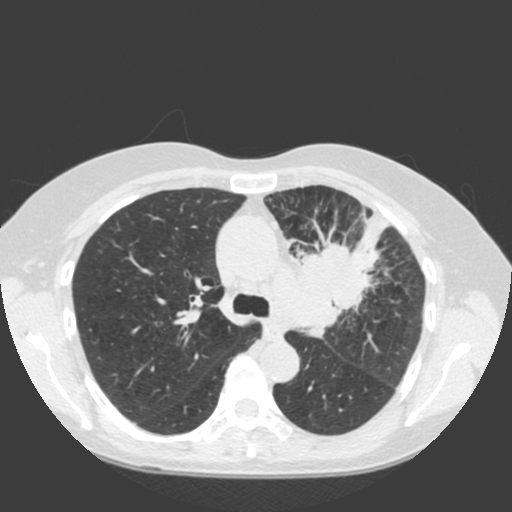
Low-dose screening chest CT, one axial slice; slice 128 of 184 in the series (ordered by position); 120 kVp; lung window (W 1500 / L -600 HU); 512 × 512 image matrix.
Outlined on this slice (expert manual segmentation):
- lesion 1 (tumor, hilum of left lung): bounding box [x1, y1, x2, y2] px = [292, 204, 388, 338]